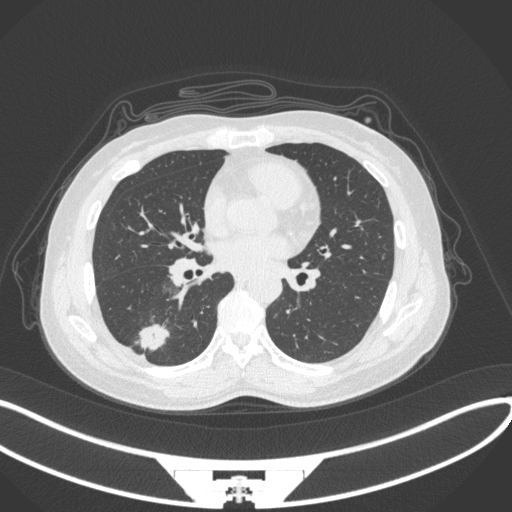
Chest CT, one axial slice; position 140 of 352 along the scan axis; 120 kVp; lung window (W 1500 / L -600 HU); 1 mm slice thickness; 512 × 512 image matrix, field of view 400 × 400 mm. Female patient, age 55 years. From the clinical record (not read from this slice): clinical TNM (as recorded): T1c N1 M0.
Annotated regions visible in this slice (rectangle marked by the reading radiologist):
- lung tumour (recorded histology: adenocarcinoma): bounding box <130,319,174,352> (left, top, right, bottom; pixels)